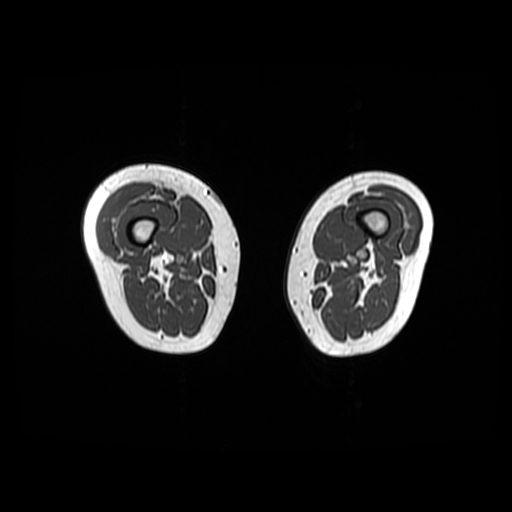
MRI of an extremity soft-tissue mass, one axial slice. Slice 10 of 48 in the series (ordered by position). 512 × 512 image matrix, field of view 440 × 440 mm. Female patient. Case-level facts recorded for this patient, not image findings: histological type: pleiomorphic undifferentiated sarcoma; grade: high; site of the primary tumour: right quadricep.
Outlined on this slice (expert manual segmentation):
- gross tumour volume including surrounding oedema: bounding box [x1, y1, x2, y2] px = [100, 183, 155, 242]